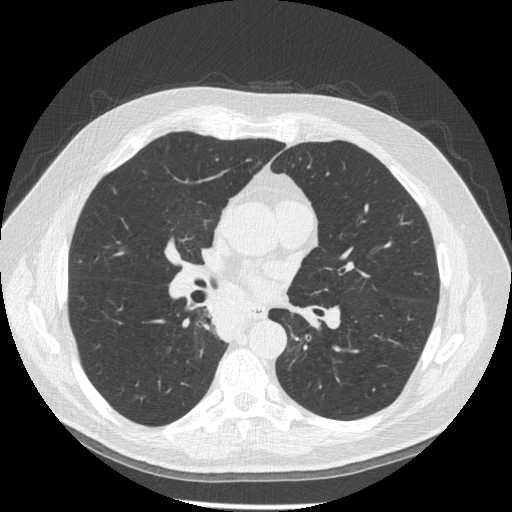
Low-dose screening chest CT, one axial slice. Slice 97 of 181 in the series (ordered by position). Reconstruction kernel STANDARD. 120 kVp. Lung window (W 1500 / L -600 HU). 512 × 512 image matrix, field of view 370 × 370 mm.
Structures marked on this image (expert manual segmentation):
- lesion 1 (tumor, lower lobe of right lung): bounding box [x1, y1, x2, y2] px = [208, 299, 246, 342]